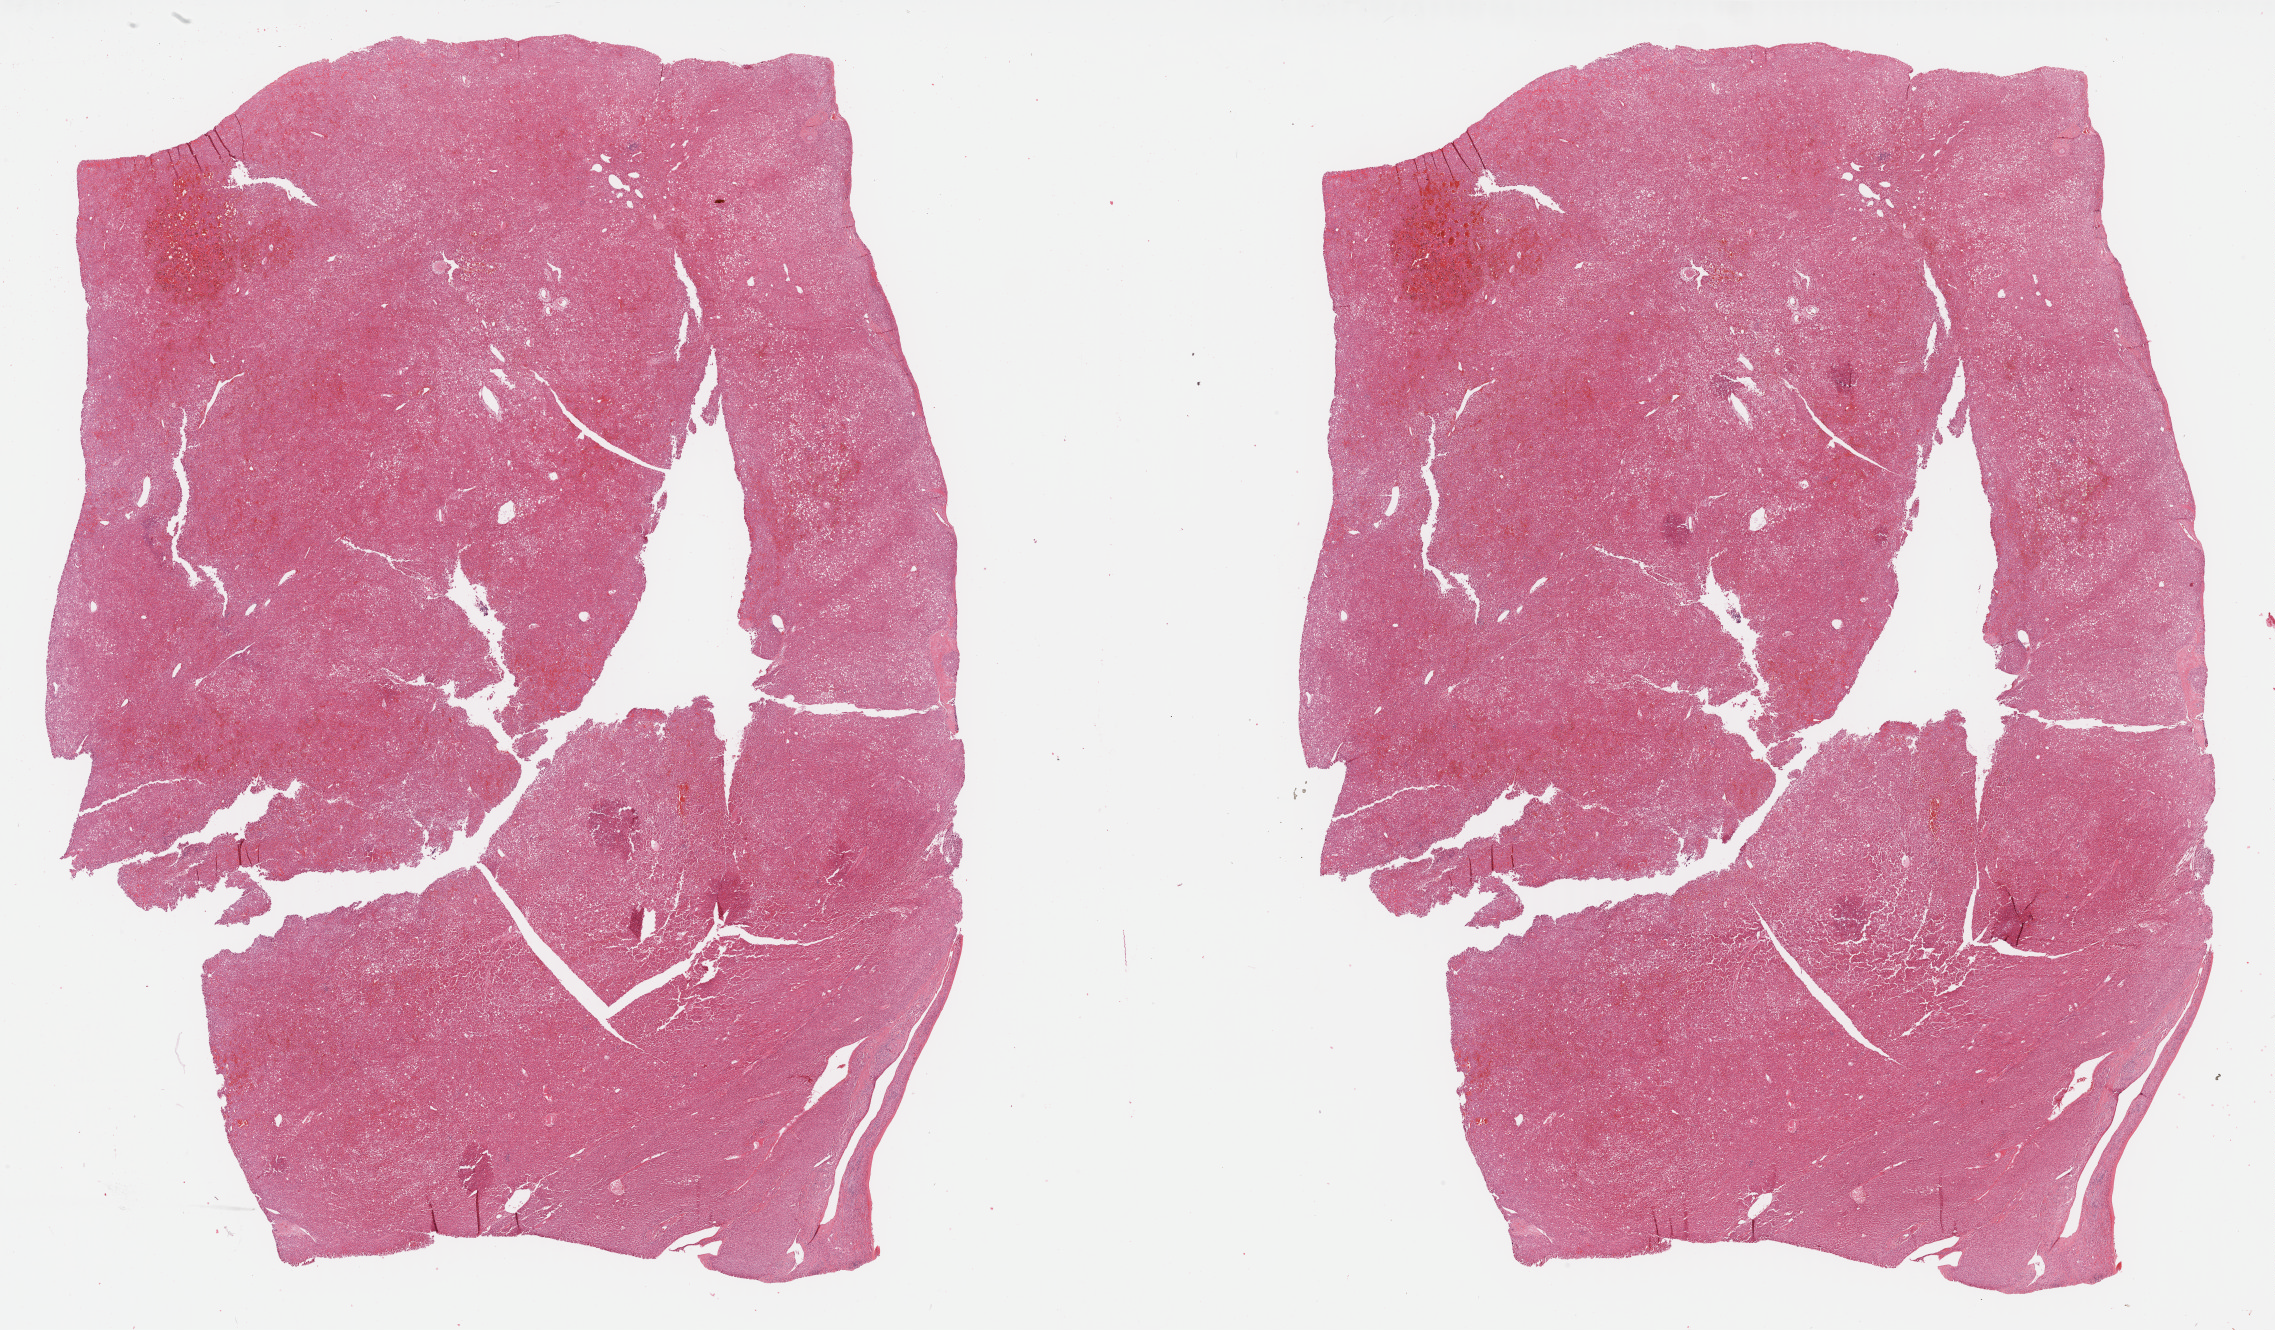
Digitized Hematoxylin and eosin (H&E) stained tissue section (whole slide) — low-resolution overview of the scanned area, about 36.8 x 21.5 mm; FFPE section; sample: primary tumour, liver. Female, age 76 years at initial diagnosis. Histologic grade: G1 (well differentiated).
- AJCC pathologic stage: I (5th edition)
- pathologic diagnosis: Hepatocellular carcinoma, NOS